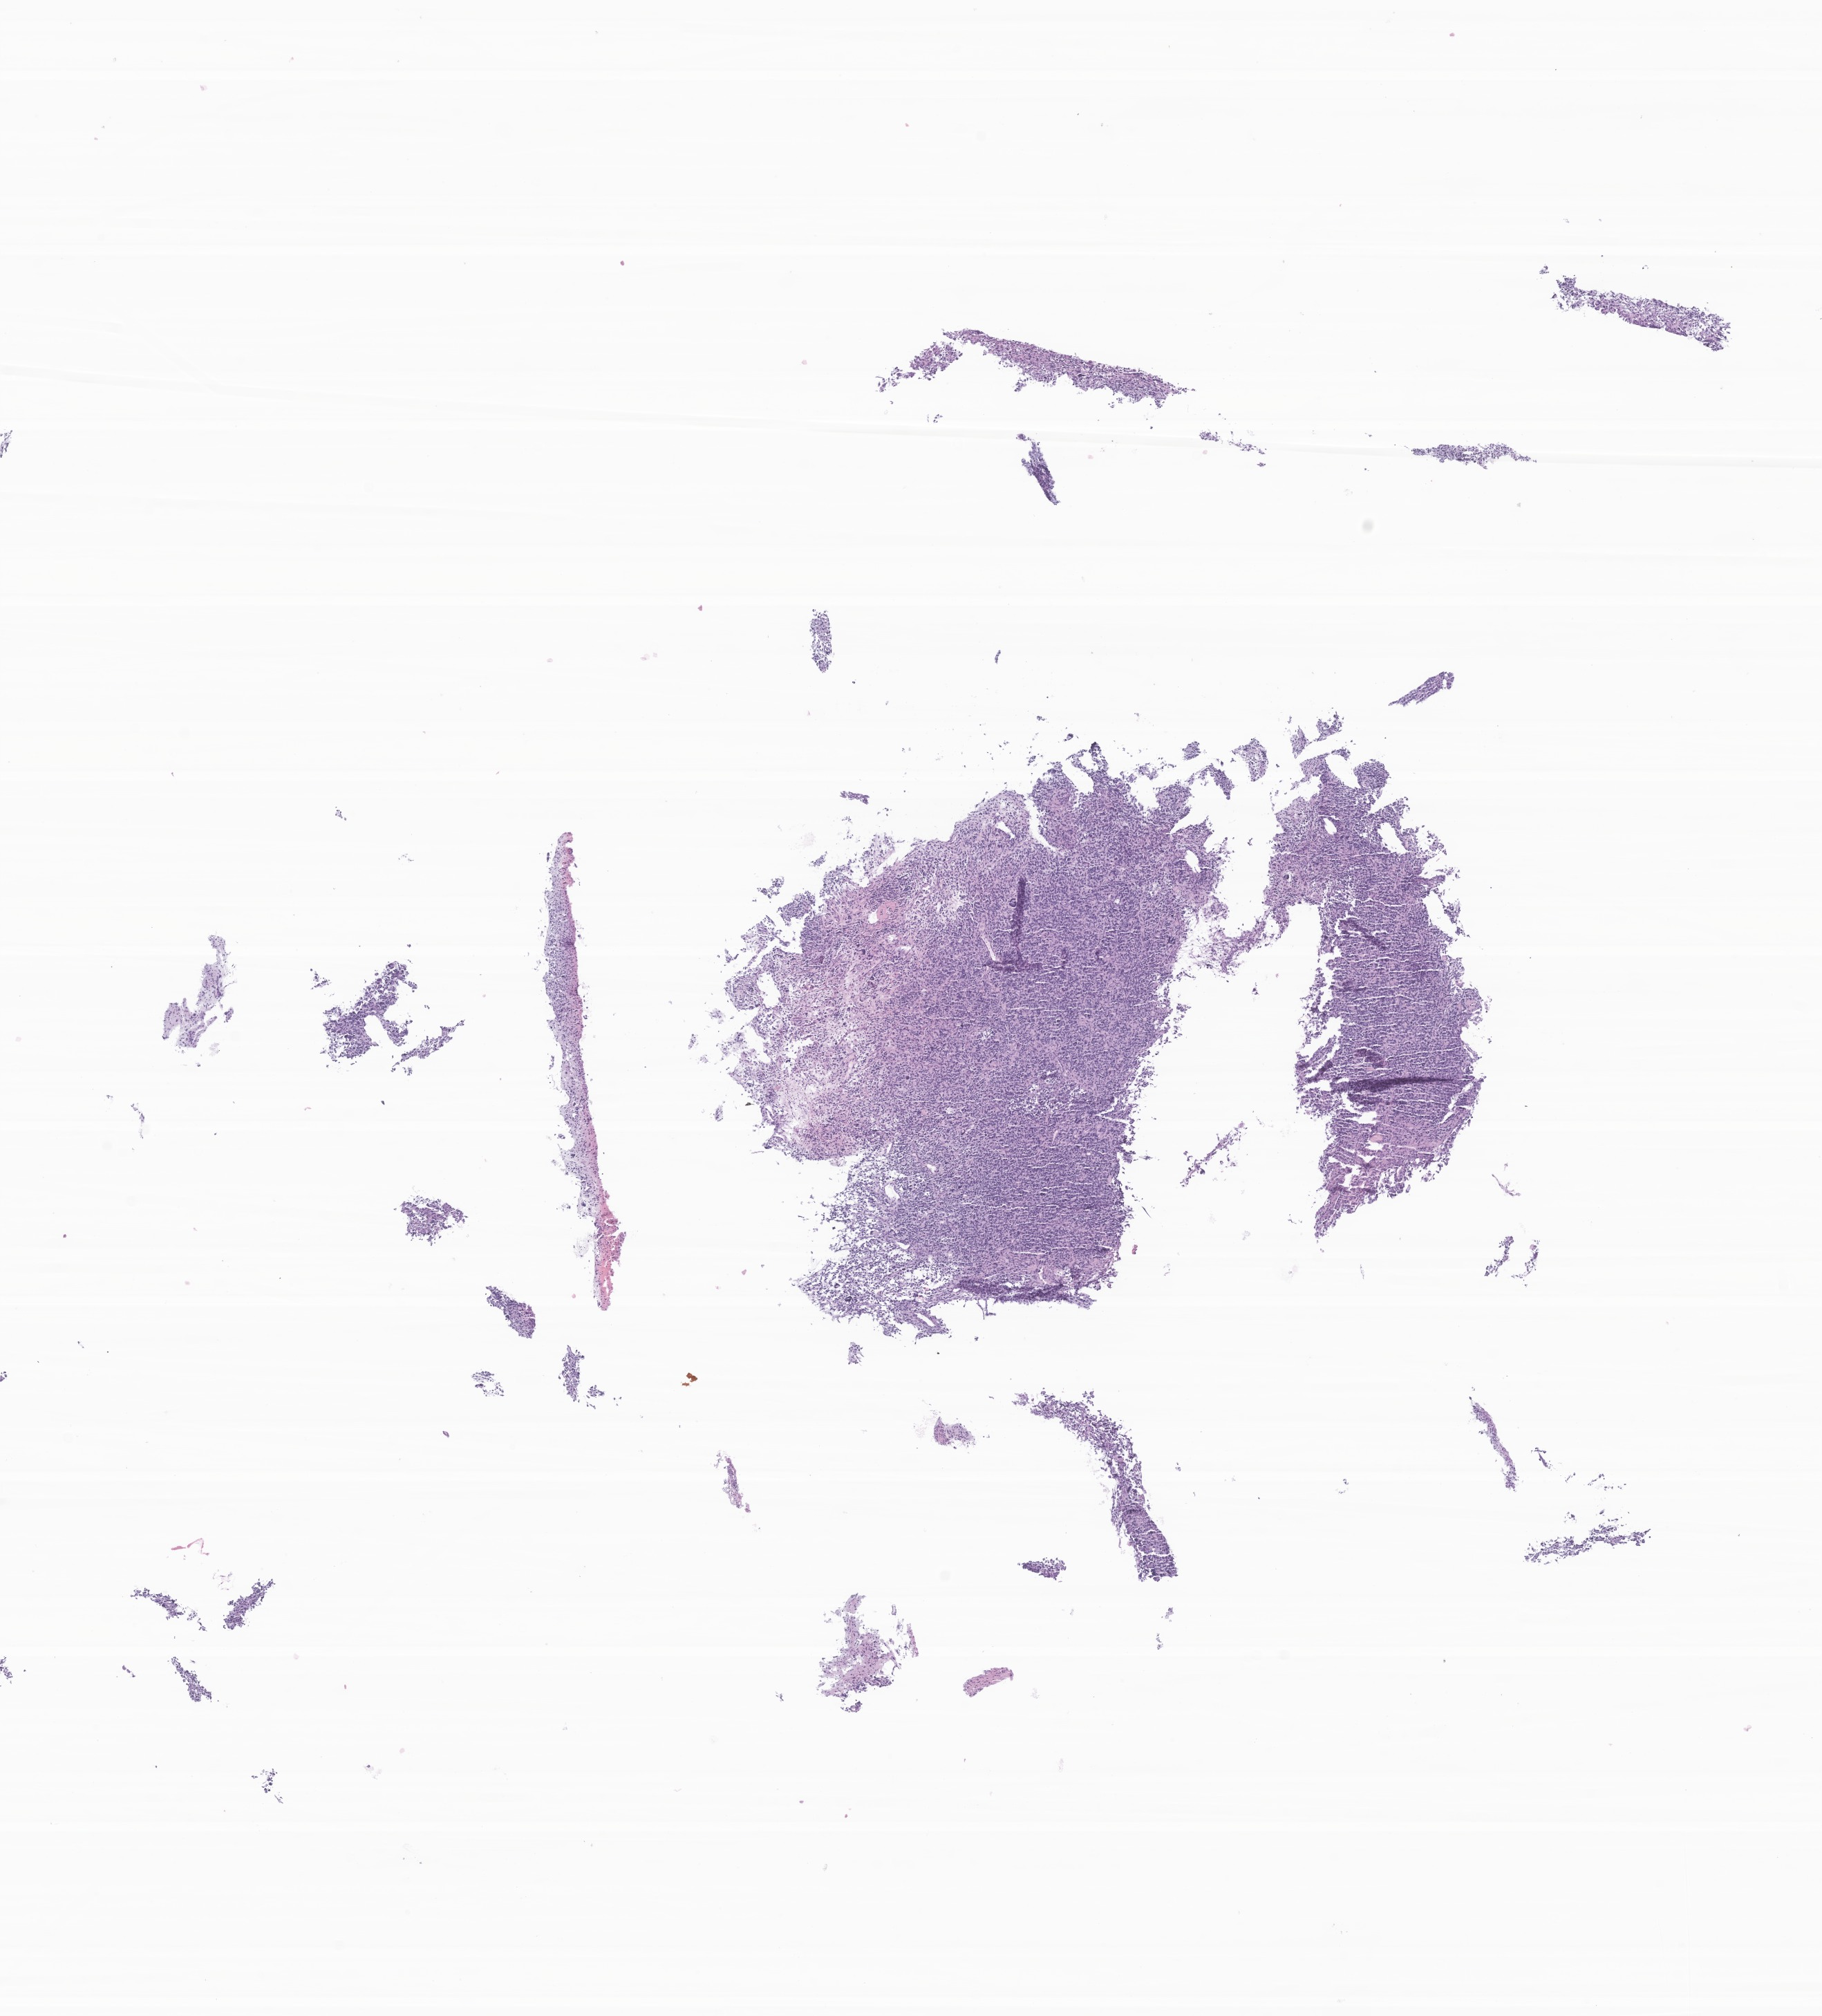
Digitized hematoxylin and eosin (H&E)-stained section of tumor tissue from the brain — a low-resolution overview of the entire scanned area, about 11.1 x 12.3 mm, formalin-fixed paraffin-embedded section. Male patient, age 208 months (17 years 4 months).
• diagnosis: Glioma, malignant